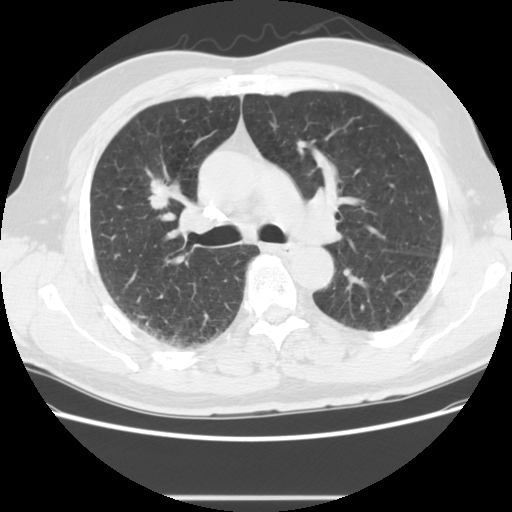
Low-dose screening chest CT, one axial slice. Position 86 of 139 along the scan axis. Reconstruction kernel STANDARD. Lung window (W 1500 / L -600 HU). 512 × 512 image matrix.
Outlined on this slice (outlined manually by an expert reader):
- lesion 1 (tumor, upper lobe of right lung): box from (x=148, y=178) to (x=173, y=210) px